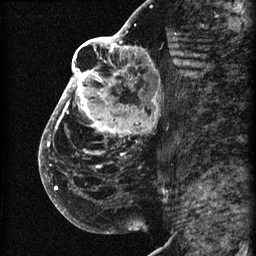
Breast MRI (dynamic contrast-enhanced), one sagittal slice. Position 35 of 60 along the scan axis. 3 images stored at this slice position (order not interpretable as contrast timing). 1.5 T. TE 4.2 ms, TR 22.7 ms. 2 mm slice thickness. 256 × 256 image matrix. Female patient, age 48 years. From the clinical record (not read from this slice): setting: breast cancer imaged before/during neoadjuvant chemotherapy; receptor status: triple-negative.
Annotated regions visible in this slice (semi-automatically segmented with operator editing):
- analysis volume of interest (the breast-tissue region the enhancement analysis was run in; not a lesion): bounding box (x1, y1, x2, y2) in pixels: (44, 30, 173, 207)
- tumour enhancement mask (voxels above the 90 % enhancement threshold inside the analysis volume of interest): (44, 30, 154, 190)